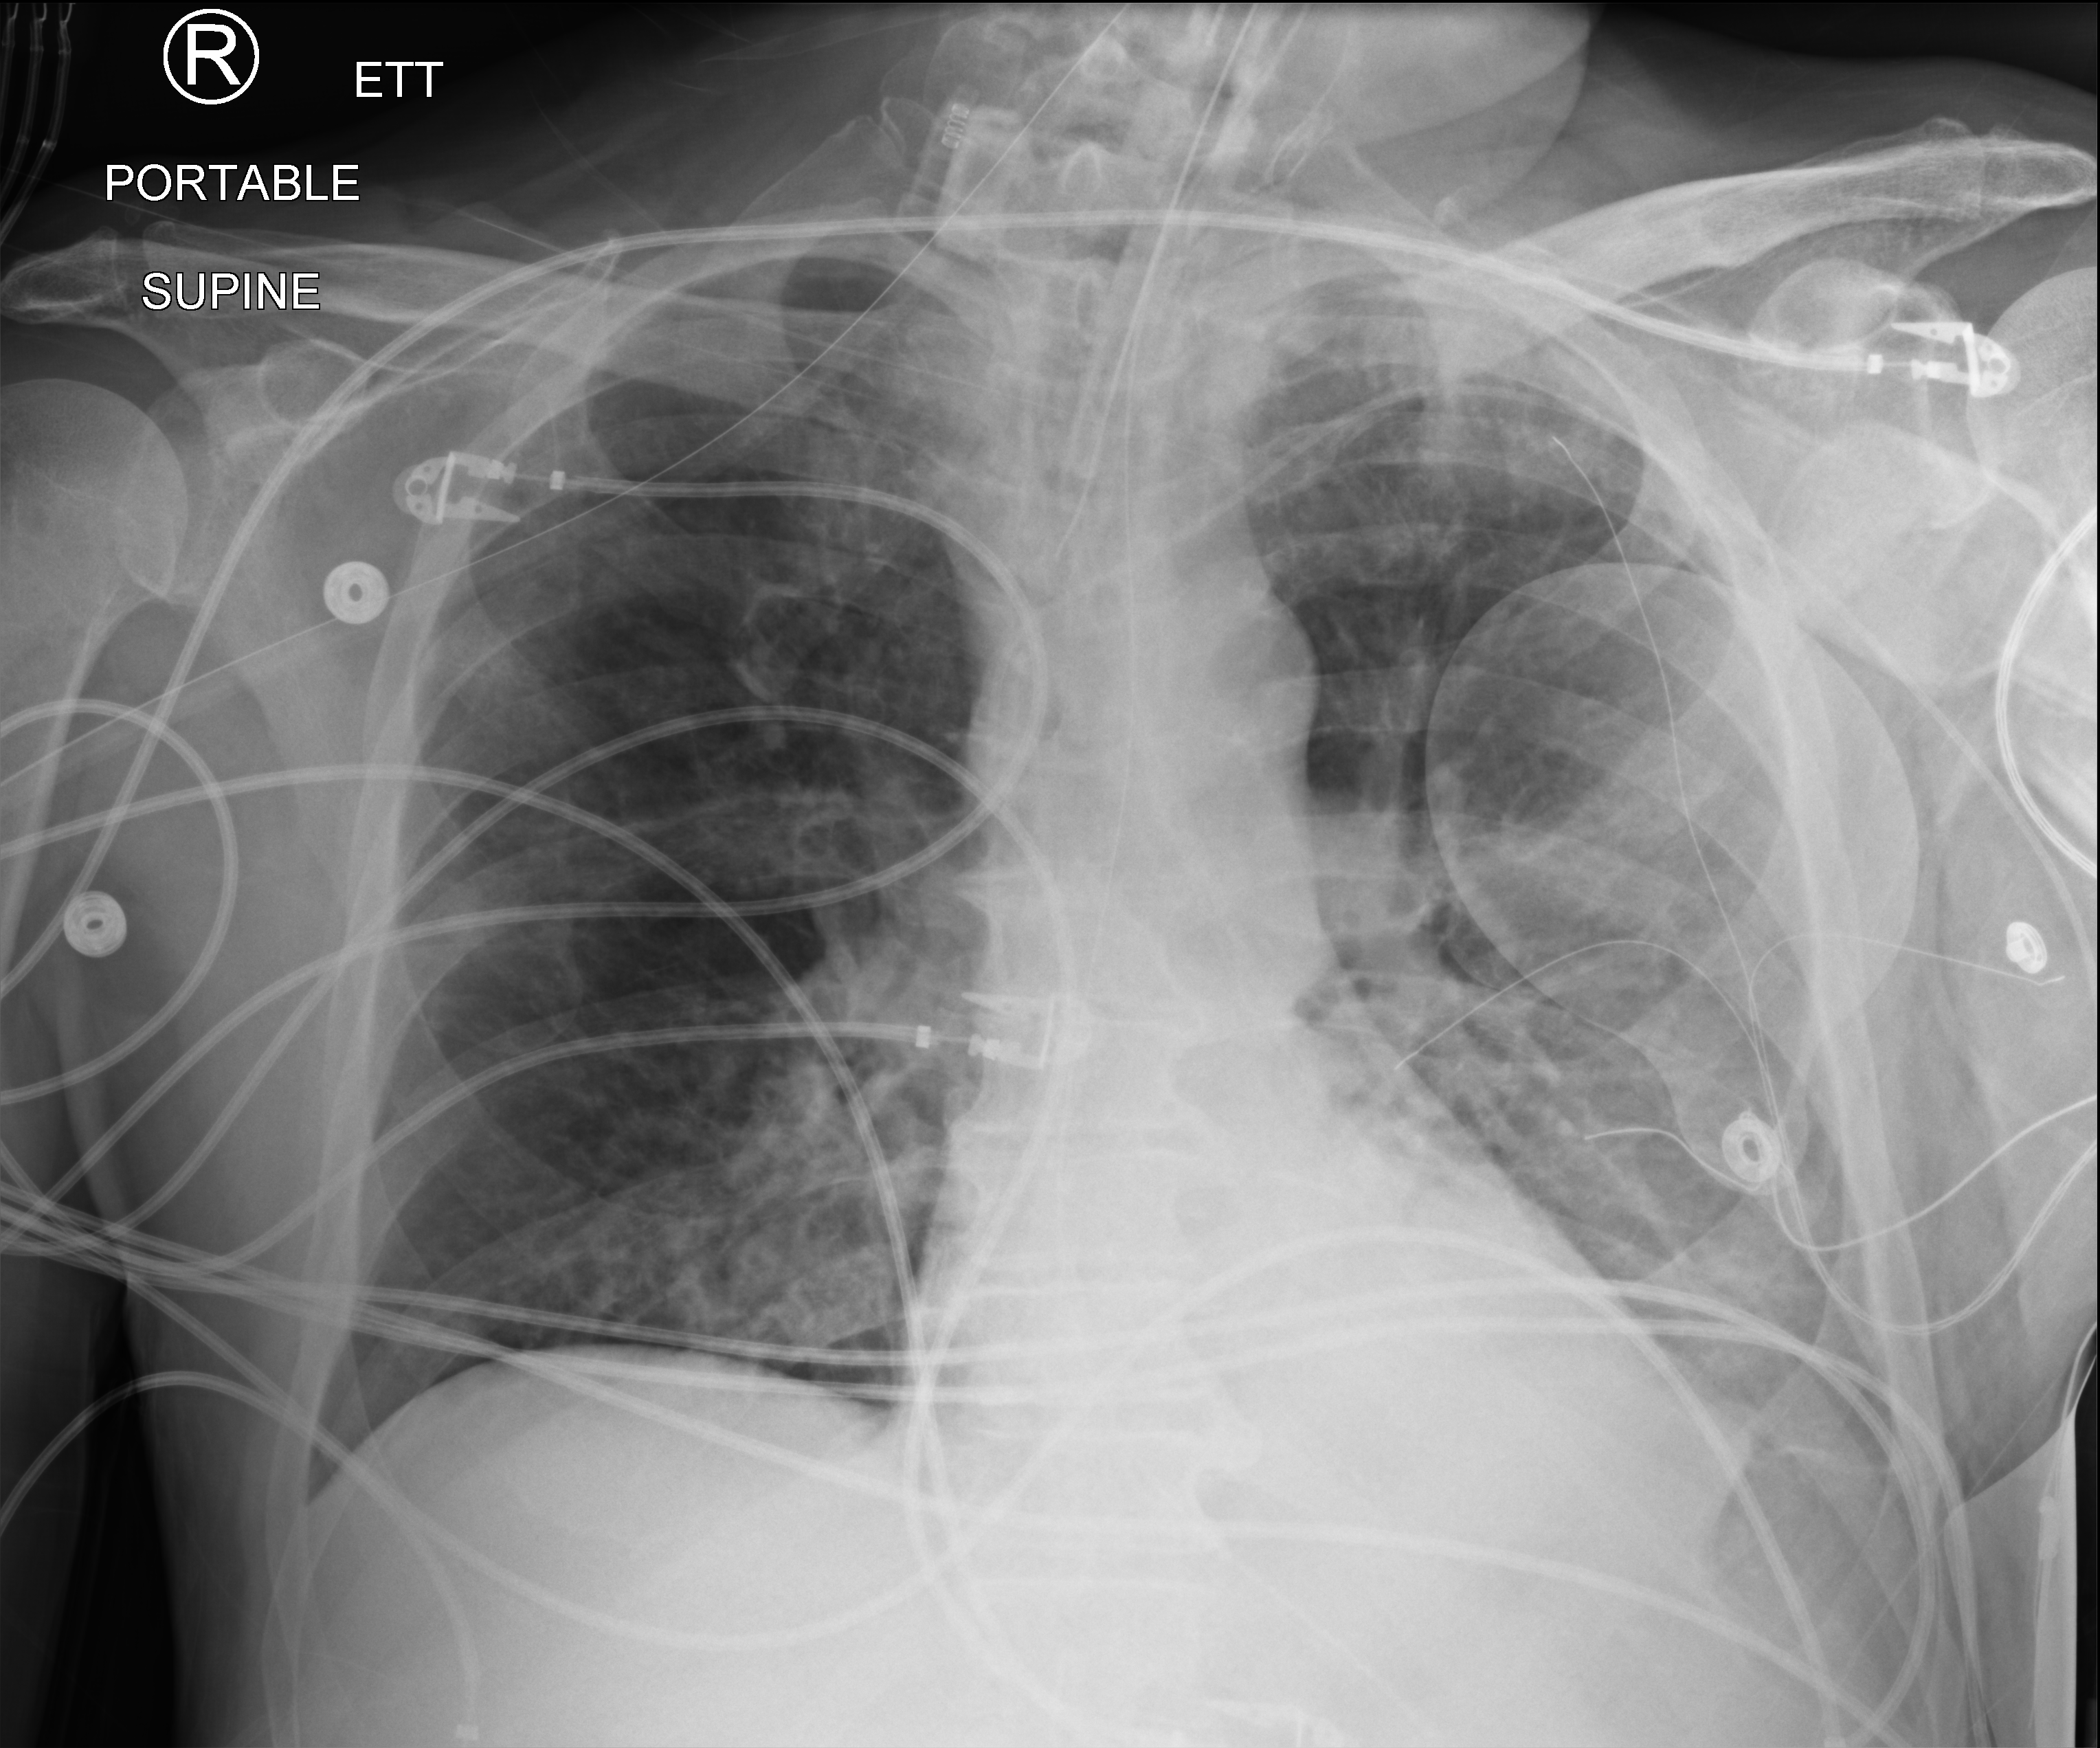
Portable chest radiograph, anteroposterior (AP) projection. Patient hospitalised with COVID-19; male, aged 60–74 years.
Hospital-stay facts (about this admission, not read from this image; timing relative to this image not recorded): diabetes (admission record): yes.